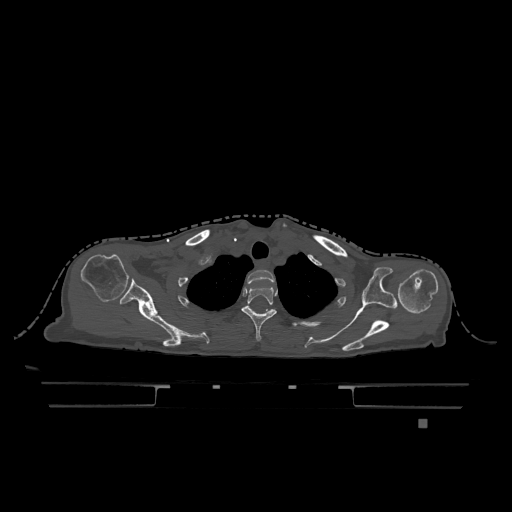
CT including the spine, one axial slice; bone window (W 1800 / L 400 HU); 0.5 mm slice thickness; 512 × 512 image matrix, field of view 500 × 500 mm. Patient: female, 74 years. From the clinical record (not read from this slice): primary cancer: lung.
Structures marked on this image (semi-automatically segmented with operator editing):
- T1 vertebra: bounding box (x1, y1, x2, y2) in pixels: (247, 270, 275, 284)
- T2 vertebra: (241, 286, 277, 341)
- T3 vertebra: (252, 310, 270, 312)